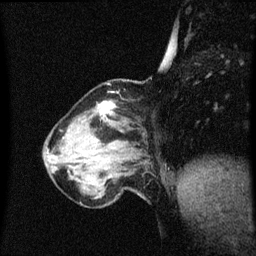
Breast MRI (dynamic contrast-enhanced), one sagittal slice. Slice 15 of 60 in the series (ordered by position). Dynamic contrast-enhanced series, image 2 of 3 at this slice position (ordered by acquisition). 1.5 T. TE 4.2 ms, TR 8.4 ms. 2 mm slice thickness. 256 × 256 image matrix, field of view 200 × 200 mm. Female patient, age 64 years. From the clinical record (not read from this slice): setting: breast cancer imaged before/during neoadjuvant chemotherapy; receptor status: HR-positive, HER2-negative.
Structures marked on this image (semi-automatic segmentation, software-assisted and operator-edited):
- analysis volume of interest (the breast-tissue region the enhancement analysis was run in; not a lesion): bounding box [x1, y1, x2, y2] px = [58, 102, 141, 167]
- tumour enhancement mask (voxels above the 70 % enhancement threshold inside the analysis volume of interest): [98, 102, 115, 113]